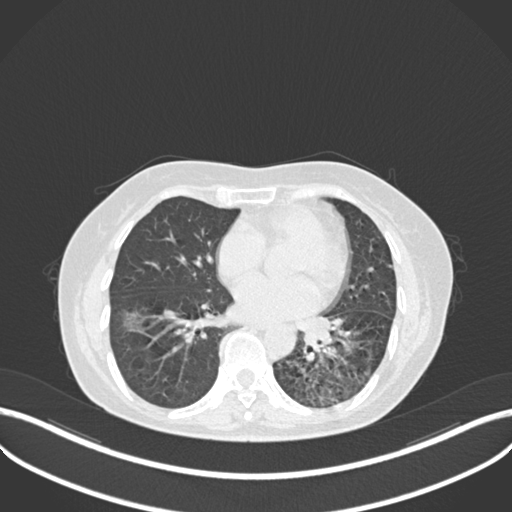
Chest CT, one axial slice; slice 110 of 270 in the series (ordered by position); 120 kVp; lung window (W 1500 / L -600 HU); 1 mm slice thickness; 512 × 512 image matrix, field of view 400 × 400 mm. Female patient, age 63 years. From the clinical record (not read from this slice): clinical TNM (as recorded): T1b N0 M0; histopathological grade: G2-3.
Annotated regions visible in this slice (rectangle marked by the reading radiologist):
- lung tumour (recorded histology: adenocarcinoma): bounding box (x1, y1, x2, y2) in pixels: (294, 312, 344, 360)